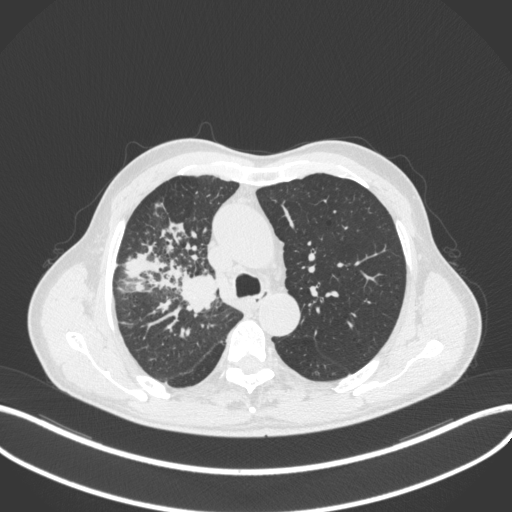
Chest CT, one axial slice. Position 336 of 490 along the scan axis. Reconstruction kernel B31f. 120 kVp. Lung window (W 1500 / L -600 HU). 1 mm slice thickness. 512 × 512 image matrix, field of view 400 × 400 mm. Male patient, age 69 years. Case-level facts recorded for this patient, not image findings: clinical TNM (as recorded): T2a N0 M0.
Structures marked on this image (bounding box drawn by a radiologist):
- lung tumour (recorded histology: adenocarcinoma): bounding box (x1, y1, x2, y2) in pixels: (178, 268, 220, 318)